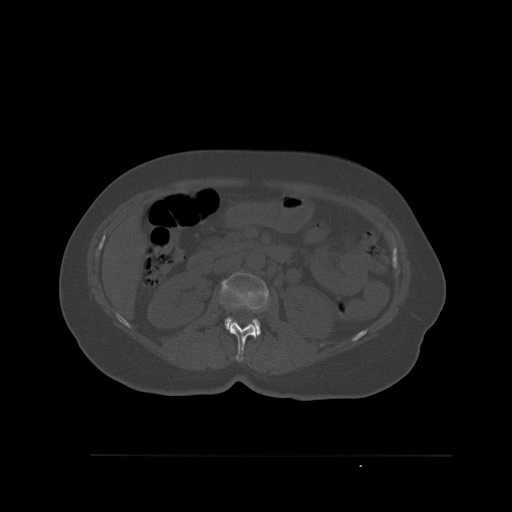
CT including the spine, one axial slice. Position 257 of 527 along the scan axis. Bone window (W 1800 / L 400 HU). 1.5 mm slice thickness. 512 × 512 image matrix, field of view 470 × 470 mm. Female patient, age 73 years. From the clinical record (not read from this slice): primary cancer: breast; vertebrae with lytic lesions (as recorded): L2.
Annotated regions visible in this slice (semi-automatically segmented with operator editing):
- L1 vertebra: bounding box [x1, y1, x2, y2] px = [229, 321, 258, 362]
- L2 vertebra: [220, 272, 270, 335]